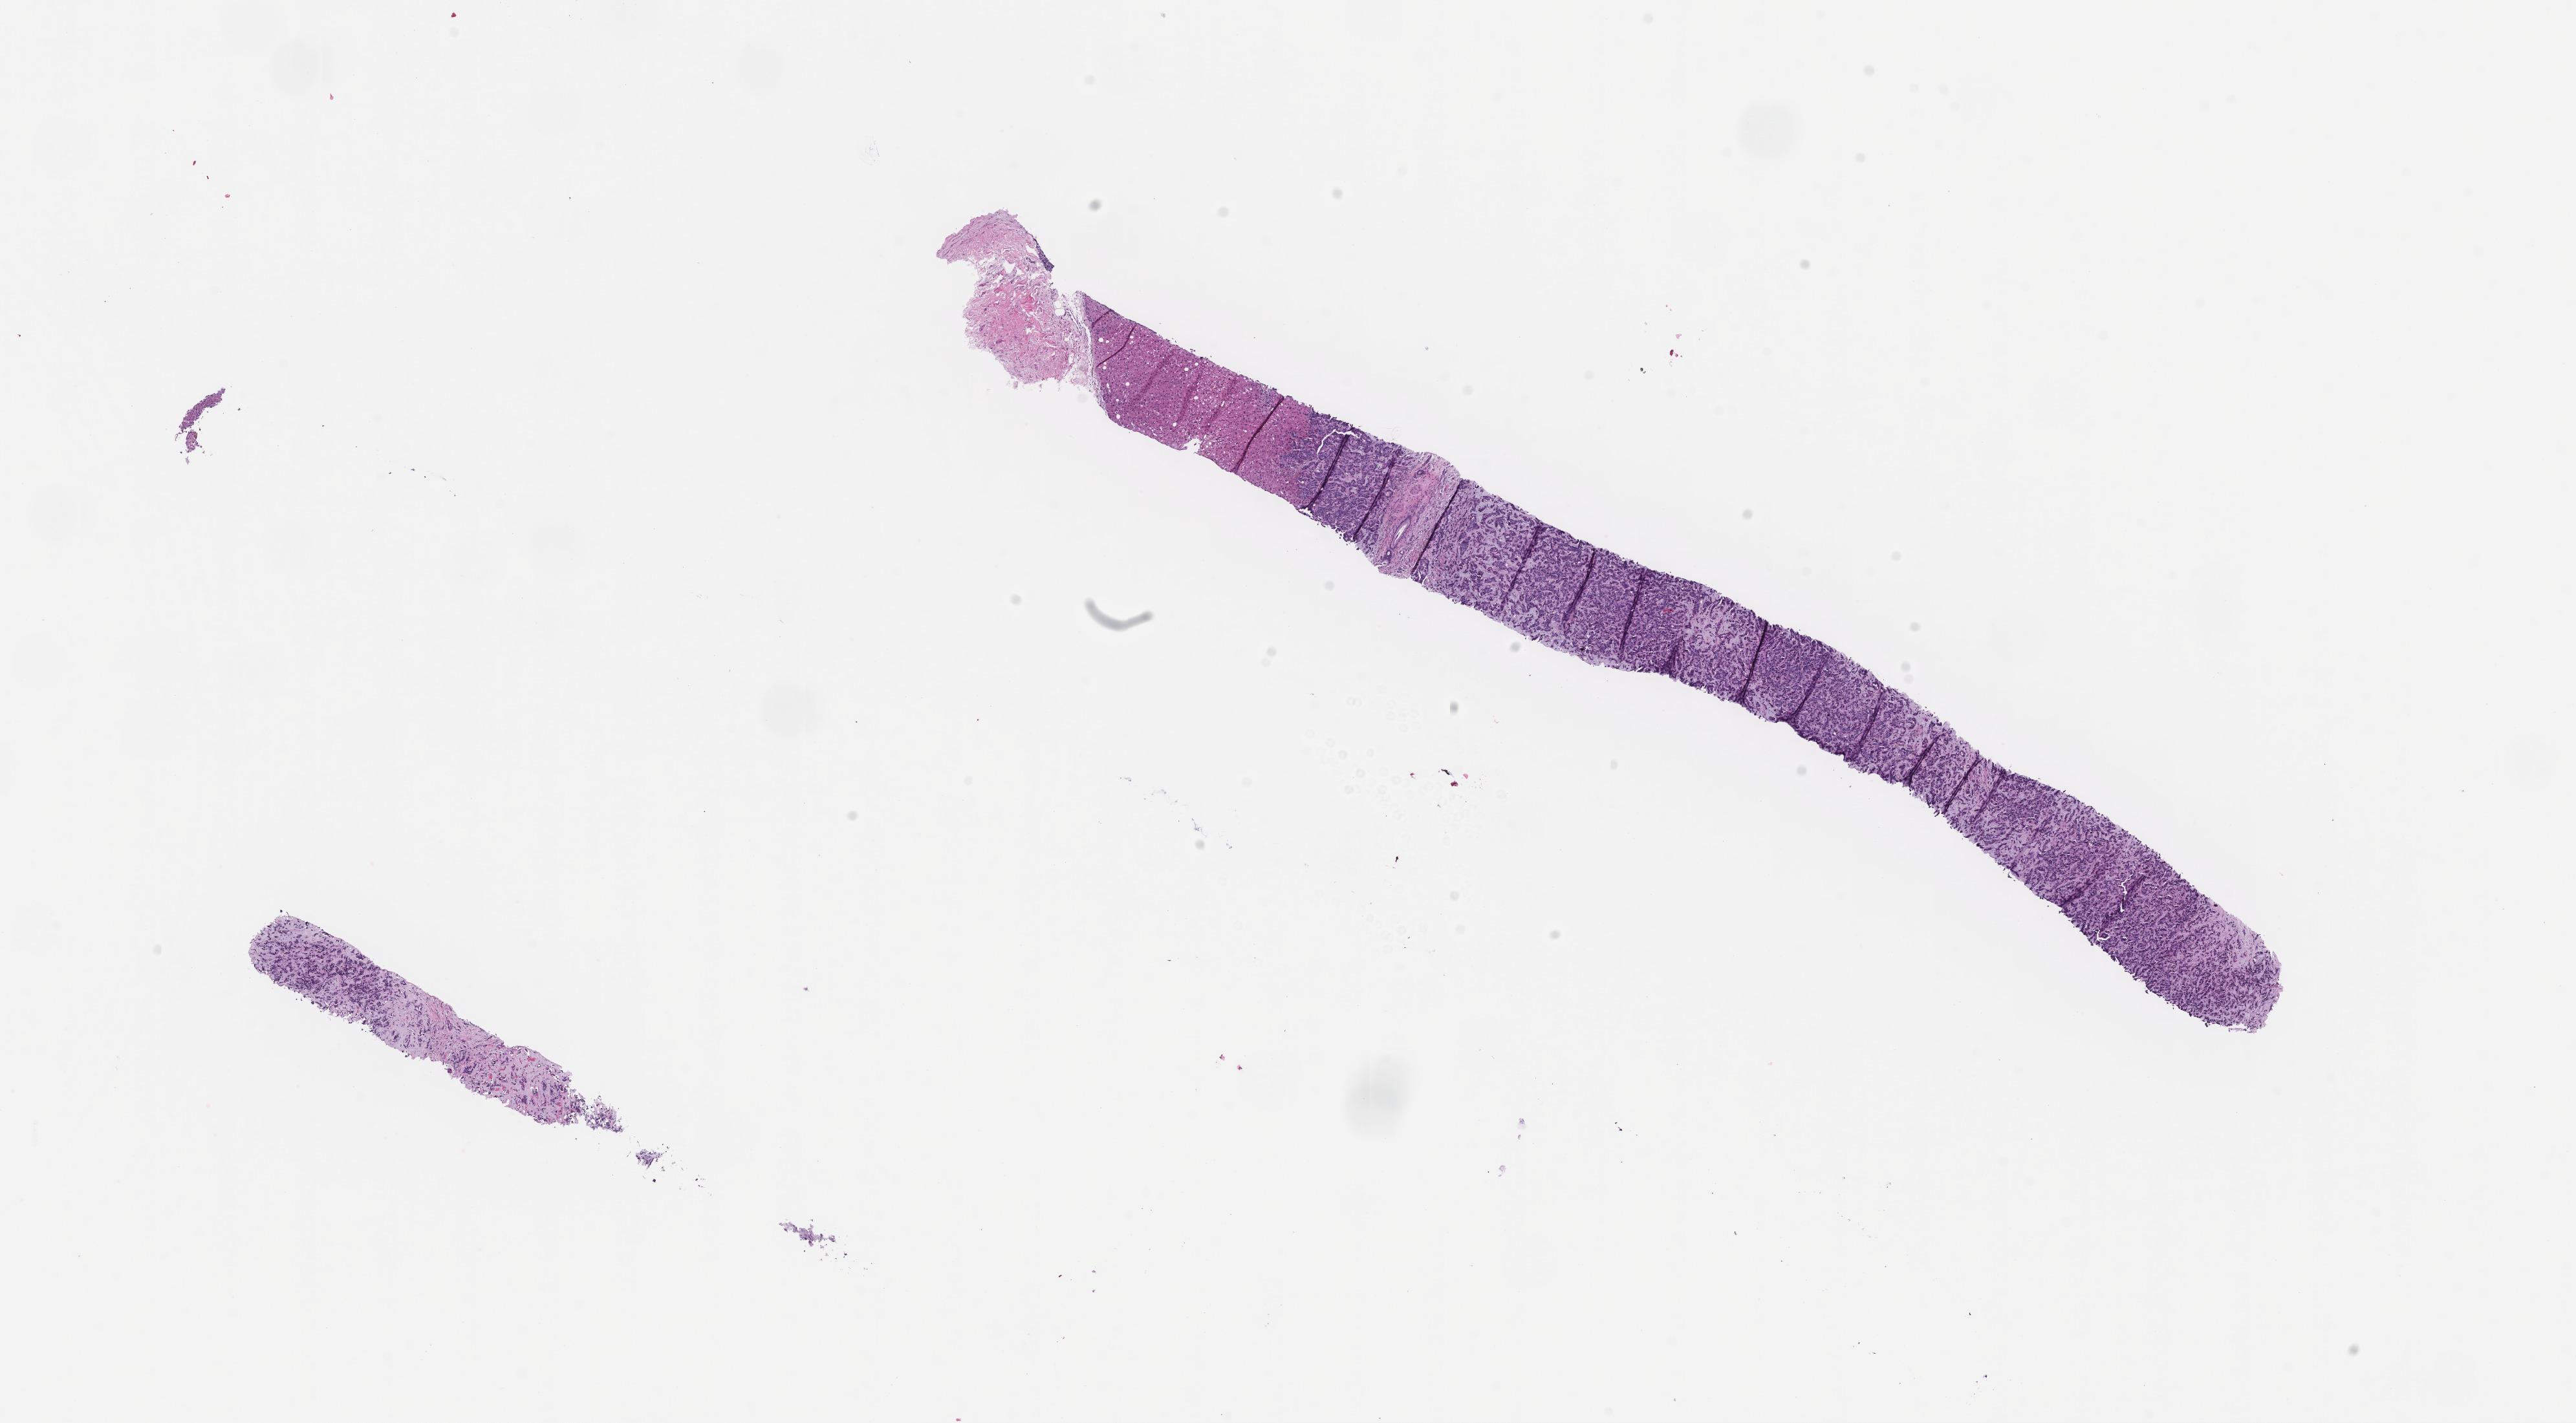
H&E whole-slide image — a low-resolution overview of the entire scanned area, about 16.1 x 8.9 mm. Formalin-fixed paraffin-embedded section. Archival tissue. Female patient.
* this section: metastatic tumor tissue
* primary diagnosis of the patient: Invasive Breast Carcinoma